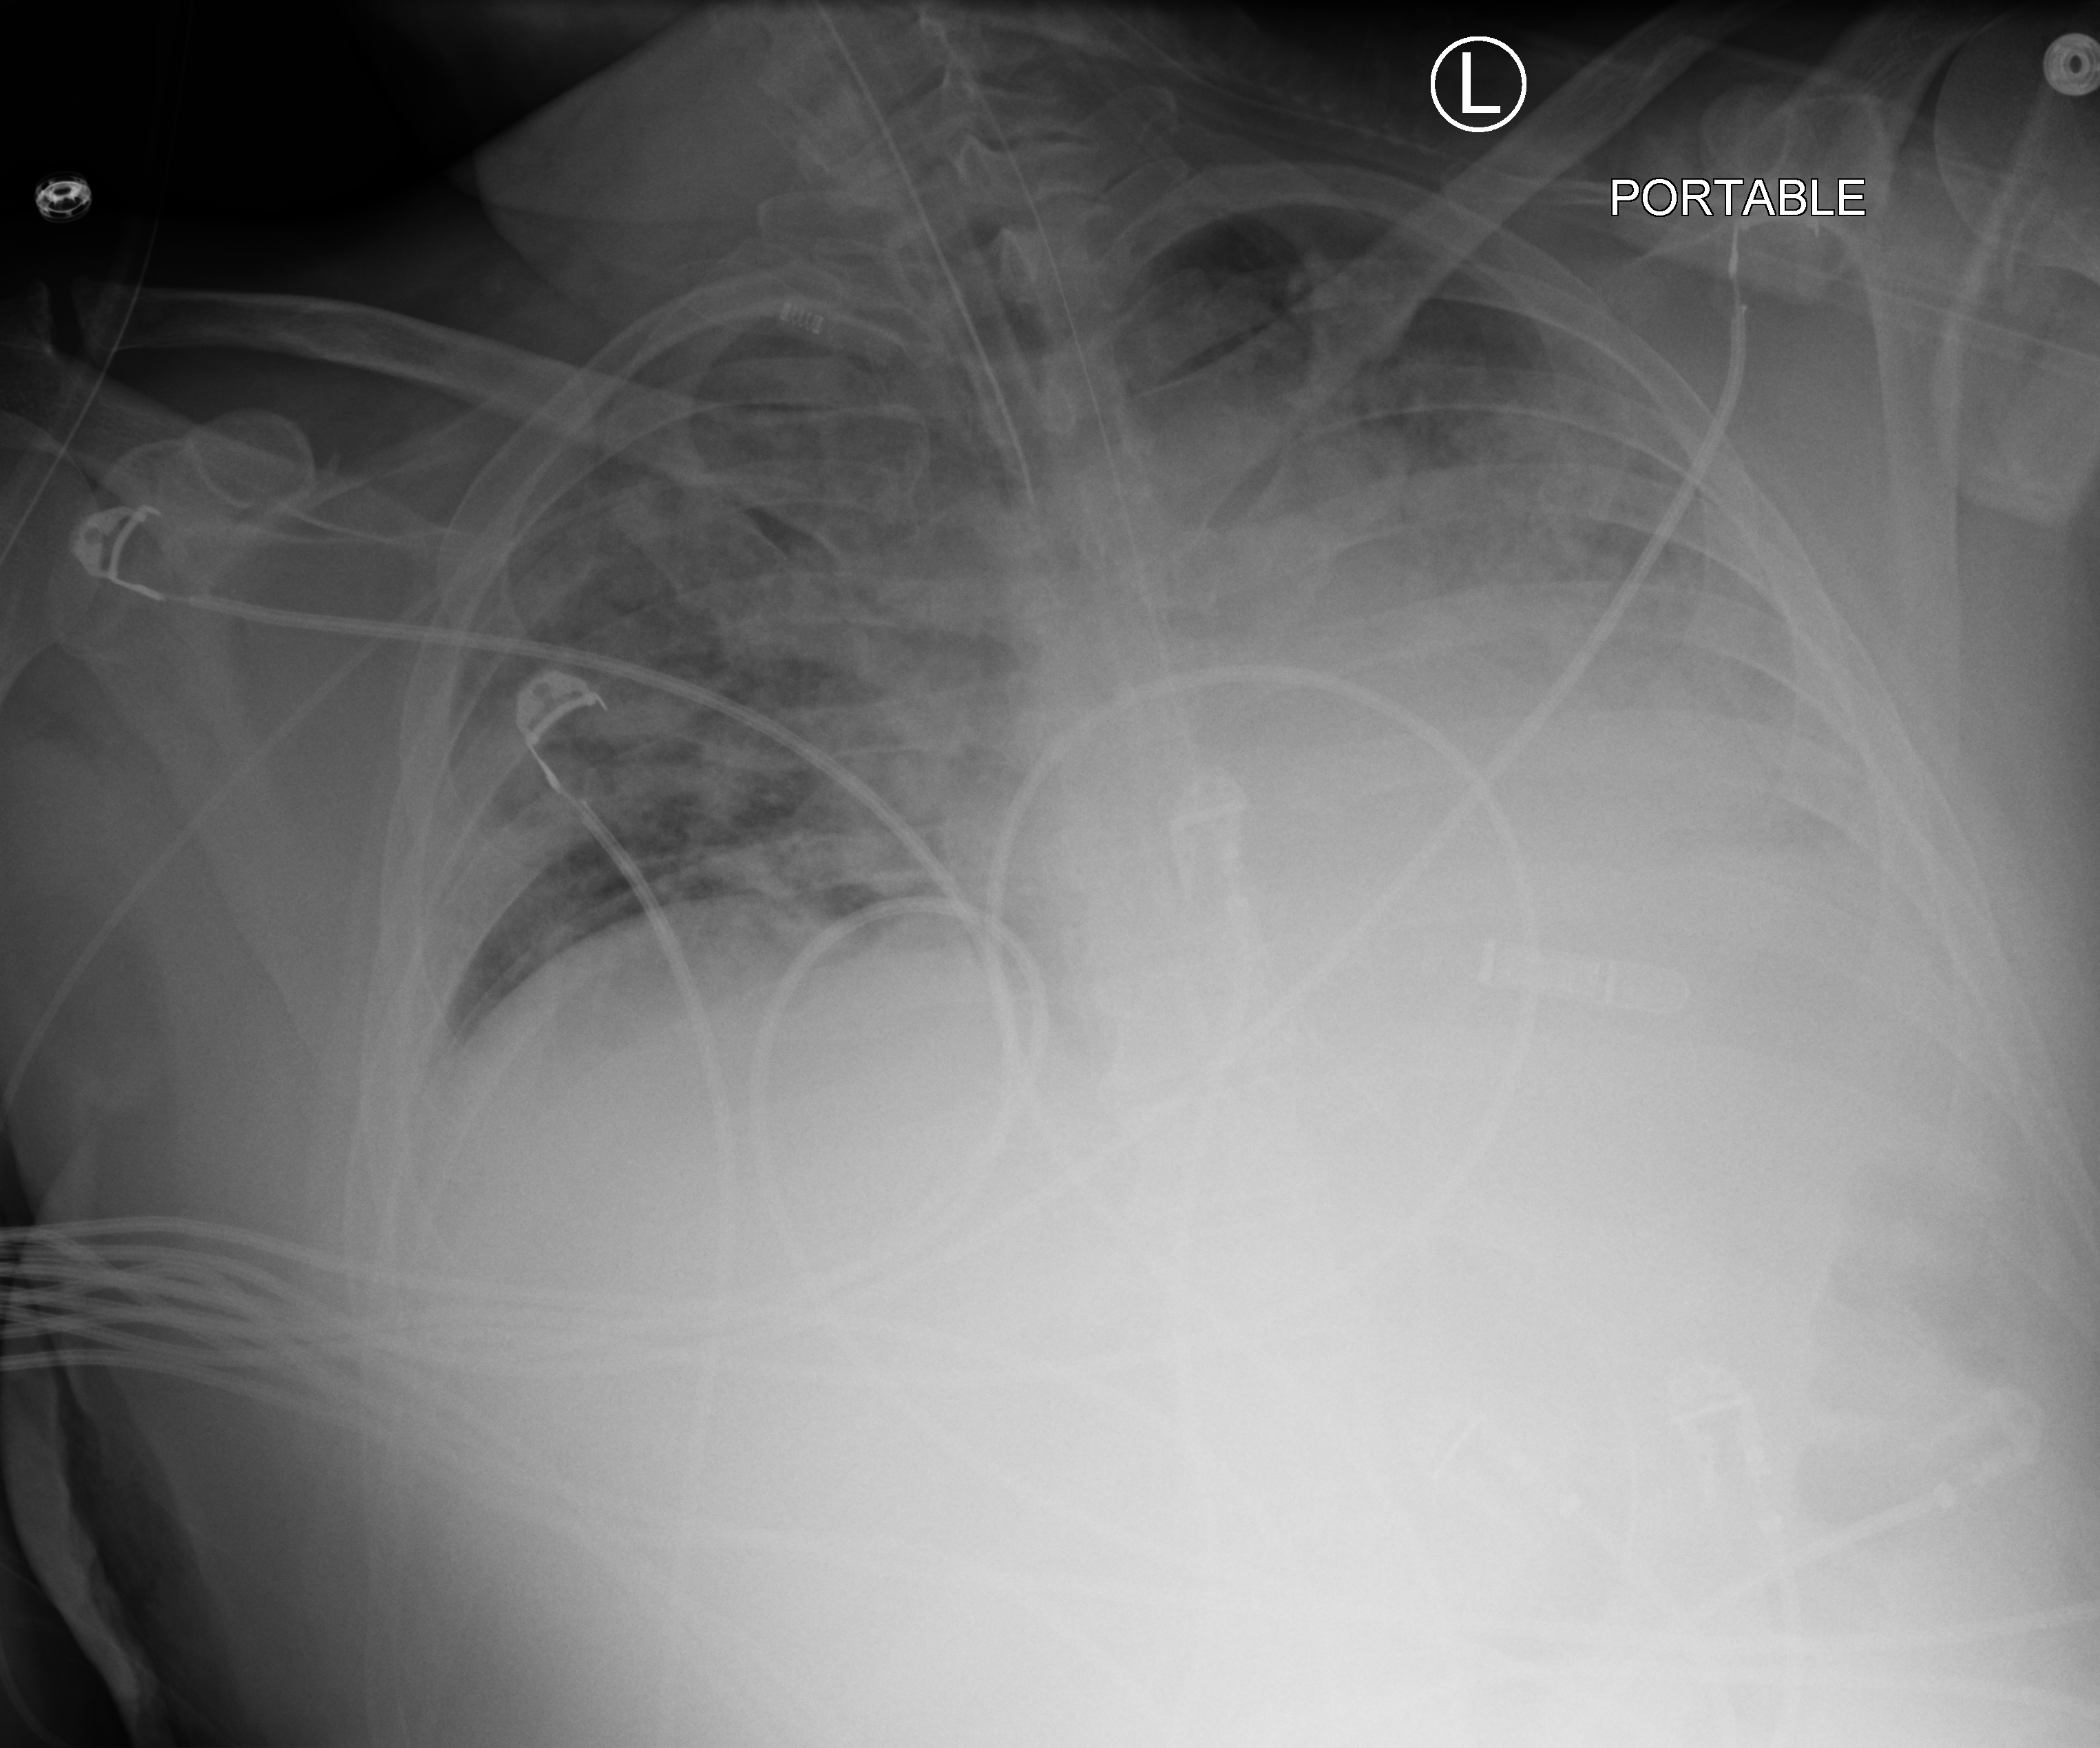
Bedside chest radiograph (computed radiography), anteroposterior (AP) projection. Male patient hospitalised with COVID-19, age 18–59 years.
Hospital-stay facts (about this admission, not read from this image; timing relative to this image not recorded):
- smoking status (admission record): former
- admitted to intensive care during this hospital stay: yes